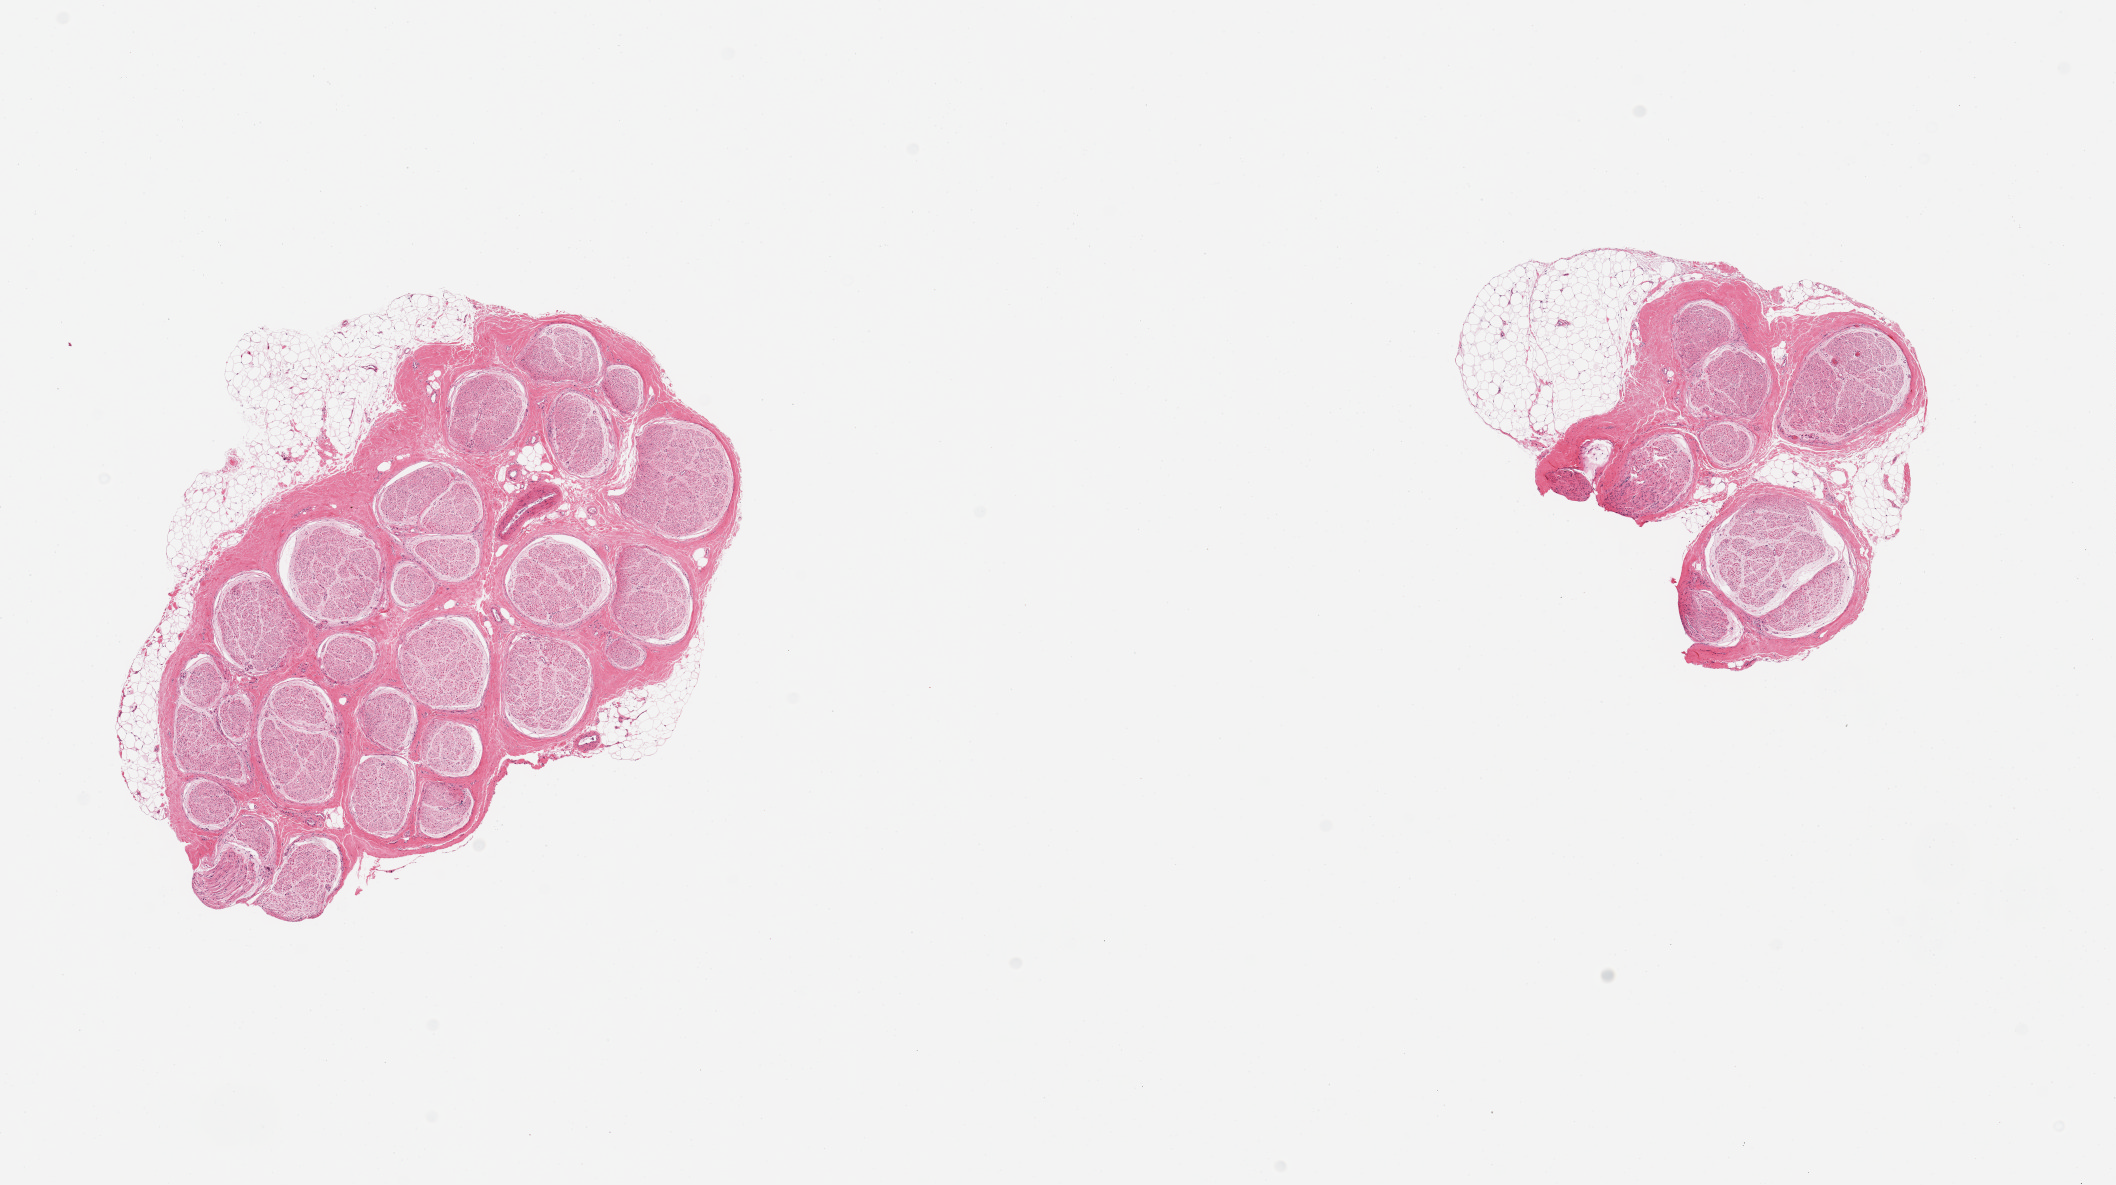
Digitized haematoxylin and eosin-stained section — whole scanned area (about 16.7 x 9.4 mm) shown as a low-resolution overview; PAXgene-fixed, paraffin-embedded tissue; section of tibial nerve (target tissue); tissue donor sample. Male donor.
Pathologist's review note for this sample: 2 pieces, adherent fat up to 1.5mm.